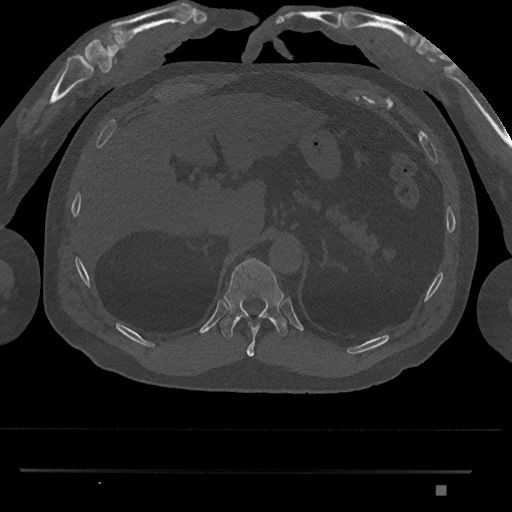
CT including the spine, one axial slice. Position 963 of 1134 along the scan axis. Reconstruction kernel Br40s/3. 120 kVp. Bone window (W 1800 / L 400 HU). 0.5 mm slice thickness. 512 × 512 image matrix. Patient: male, 65 years. Case-level facts recorded for this patient, not image findings: primary cancer: prostate.
Structures marked on this image (semi-automatic segmentation, software-assisted and operator-edited):
- T10 vertebra: bounding box [x1, y1, x2, y2] px = [246, 322, 260, 357]
- T11 vertebra: [220, 258, 288, 340]